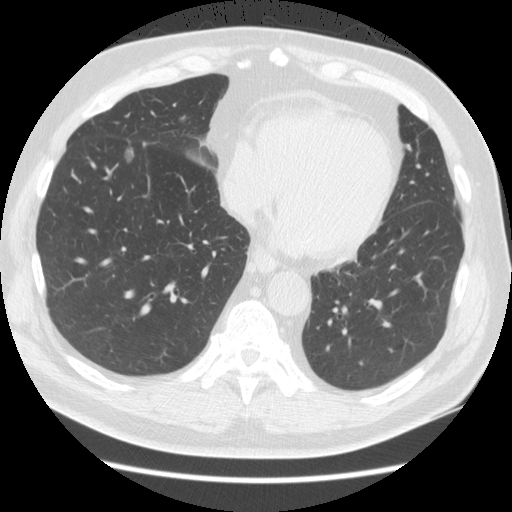
Low-dose screening chest CT, one axial slice; position 54 of 161 along the scan axis; lung window (W 1500 / L -600 HU); 512 × 512 image matrix, field of view 360 × 360 mm.
Outlined on this slice (outlined manually by an expert reader):
- lesion 1 (tumor, lower lobe of right lung): bounding box (x1, y1, x2, y2) in pixels: (127, 149, 133, 157)